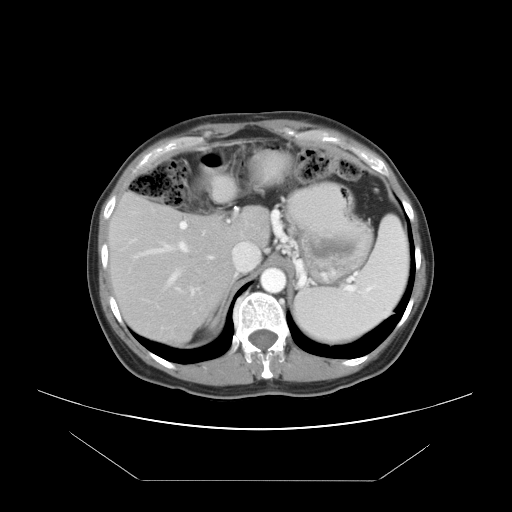
Contrast-enhanced abdominal CT, one axial slice. Position 32 of 45 along the scan axis. 120 kVp. Intravenous contrast given. Soft-tissue window (W 400 / L 40 HU). 512 × 512 image matrix, field of view 405 × 405 mm. Female patient, age 52 years. Case-level facts recorded for this patient, not image findings: diagnosis: colorectal cancer liver metastases, imaged before liver resection; multiple liver metastases: yes; largest metastasis: 2.5 cm; disease in both lobes: no.
Outlined on this slice (manually delineated by an expert):
- hepatic veins: bounding box [x1, y1, x2, y2] px = [132, 240, 200, 303]
- liver: [111, 195, 269, 343]
- planned liver remnant (the part of the liver to remain after resection): [111, 195, 269, 325]
- portal vein (with intrahepatic branches): [179, 220, 230, 294]